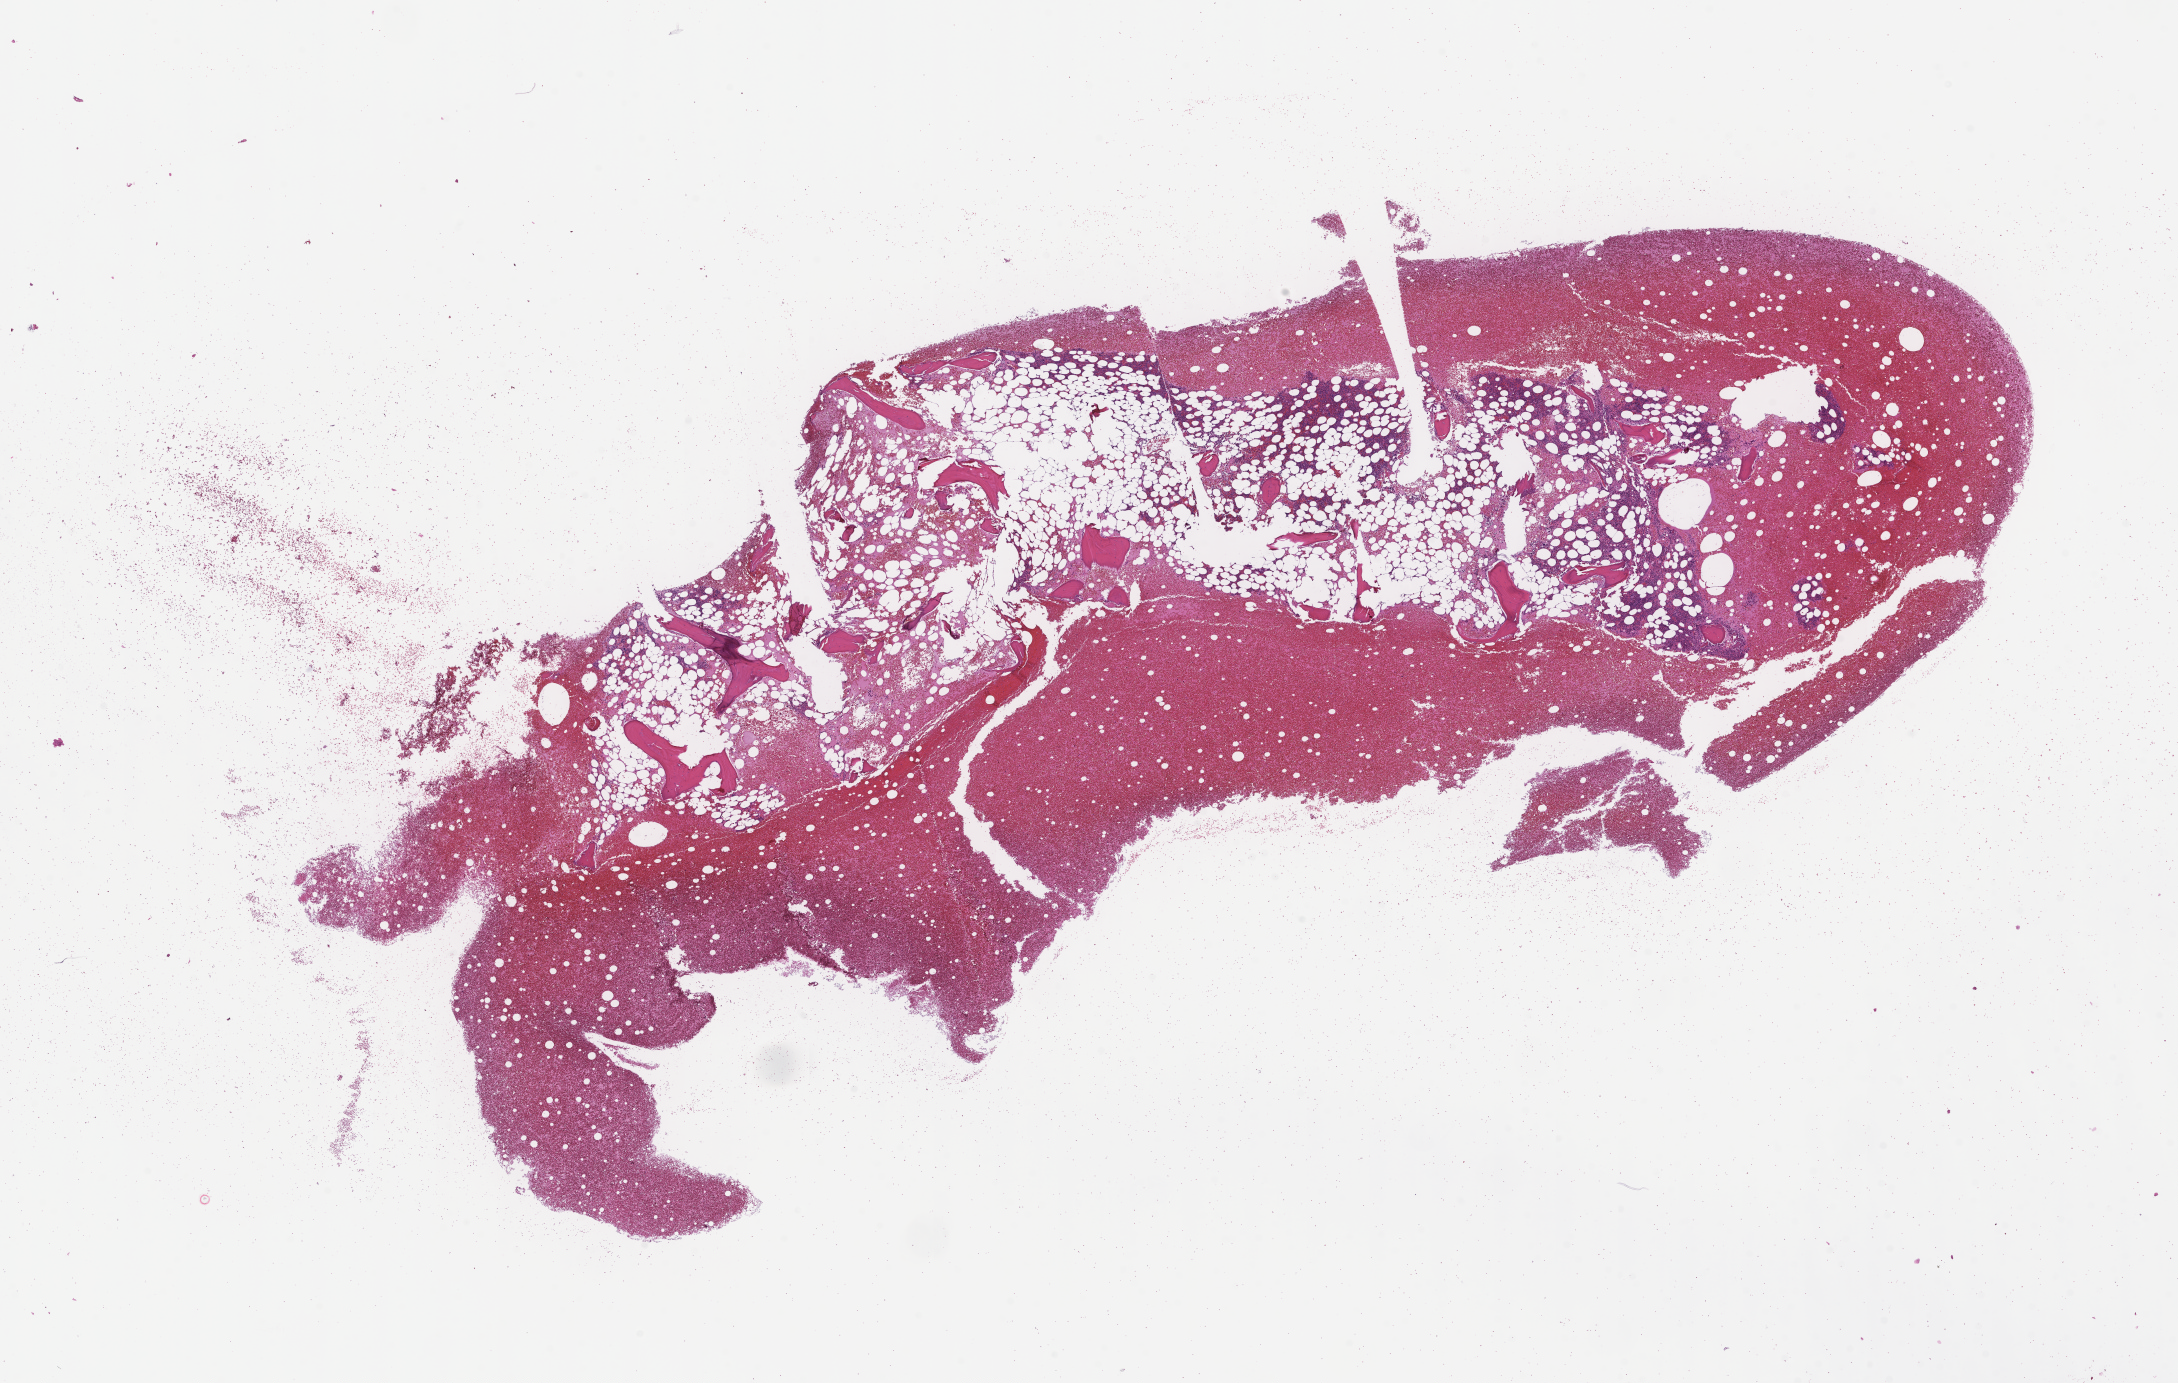
Digitized hematoxylin and eosin (H&E)-stained section — shown as a low-resolution overview of the whole scanned area (about 17.6 x 11.2 mm). FFPE section. Site: bone. Specimen time point: archival tissue. Male patient.
This section: primary tumour tissue. Diagnosis: Plasma Cell Myeloma.